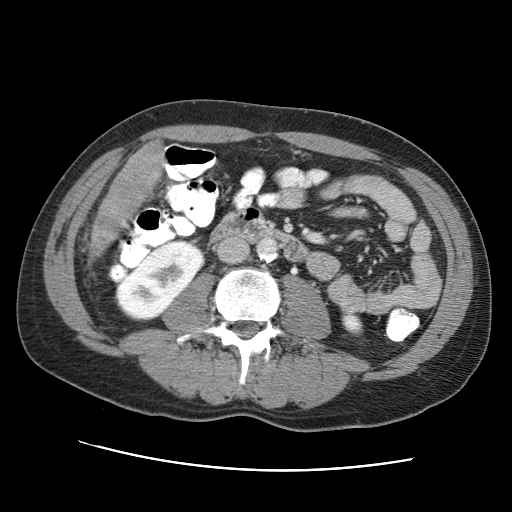
Contrast-enhanced abdominal CT (liver protocol), one axial slice; slice 9 of 95 in the series (ordered by position); reconstruction kernel STANDARD; 120 kVp; one of 2 acquisitions stored at this slice position; soft-tissue window (W 400 / L 40 HU); 512 × 512 image matrix. Case-level facts recorded for this patient, not image findings: diagnosis: hepatocellular carcinoma (patient treated with transarterial chemoembolisation; whether this scan precedes or follows treatment is not stated here); TNM stage (as recorded): Stage-IVA; Child-Pugh class: A; tumour nodularity: multinodular.
Structures marked on this image (semi-automatically segmented with operator editing):
- liver parenchyma outside the tumour (the mass and vessels are separate outlines, so this box may not span the whole liver): box from (x=92, y=144) to (x=163, y=226) px
- mass: (x=89, y=174)–(x=154, y=259)